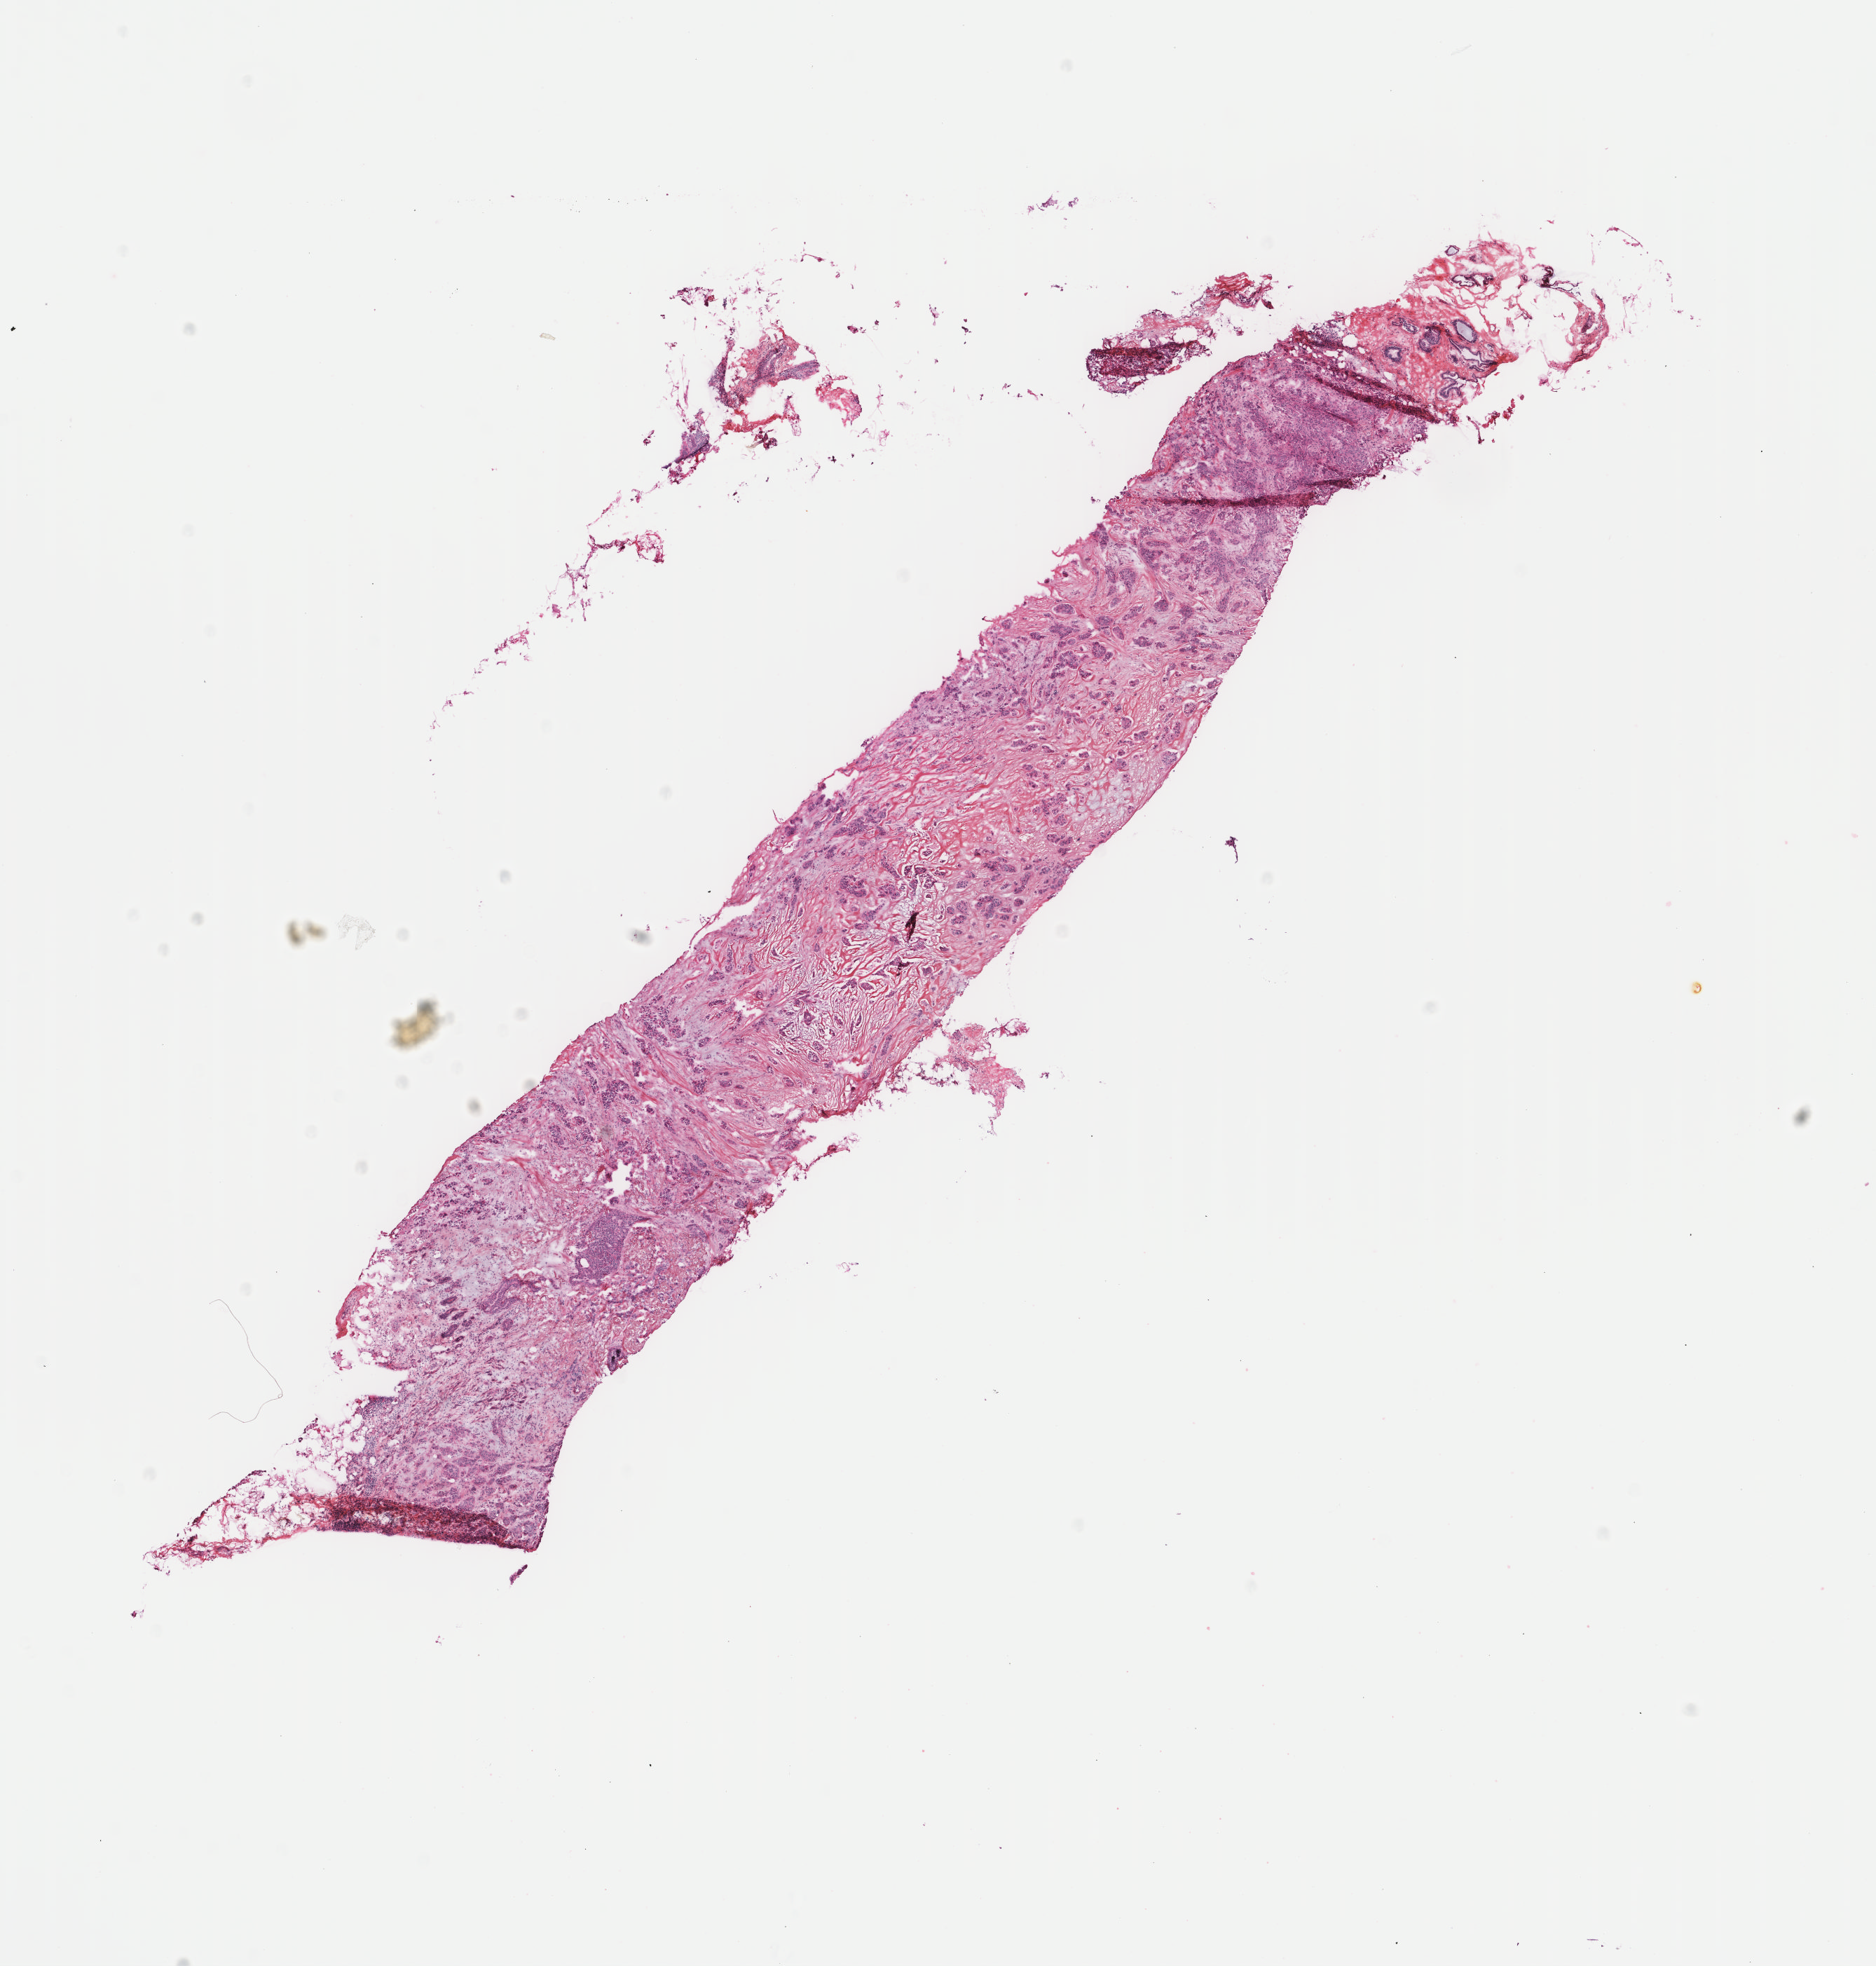
Whole-slide histology image, Hematoxylin and eosin (H&E) stained — shown as a low-resolution overview of the whole scanned area (about 10.6 x 11.1 mm, acquisition: 40x scan). Frozen section from the top of the tissue portion. Breast, primary tumour sample. Female patient; age at initial diagnosis 47 years. Composition of this section per pathologist review: tumour cells 90%, tumour nuclei 85%, normal cells 8%, stromal cells 2%, necrosis 0%. Inflammatory infiltration, as recorded: lymphocyte infiltration 0%, monocyte infiltration 0%, neutrophil infiltration 0%.
• lymph nodes positive (case pathology): 1 of 4 examined
• AJCC pathologic stage: IIA (6th edition)
• laterality: left
• diagnosis: Infiltrating duct carcinoma, NOS